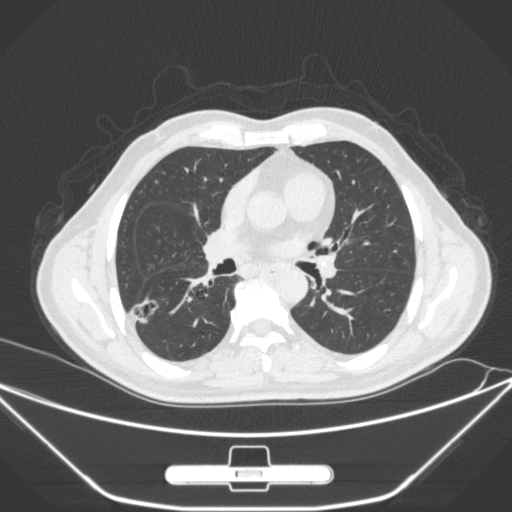
Chest CT, one axial slice; position 153 of 310 along the scan axis; lung window (W 1500 / L -600 HU); 1 mm slice thickness; 512 × 512 image matrix, field of view 398 × 398 mm. Patient: male, 71 years. From the clinical record (not read from this slice): clinical TNM (as recorded): T1c N0 M0; histopathological grade: G2.
Structures marked on this image (rectangle marked by the reading radiologist):
- lung tumour (recorded histology: adenocarcinoma): bounding box (x1, y1, x2, y2) in pixels: (121, 294, 166, 329)